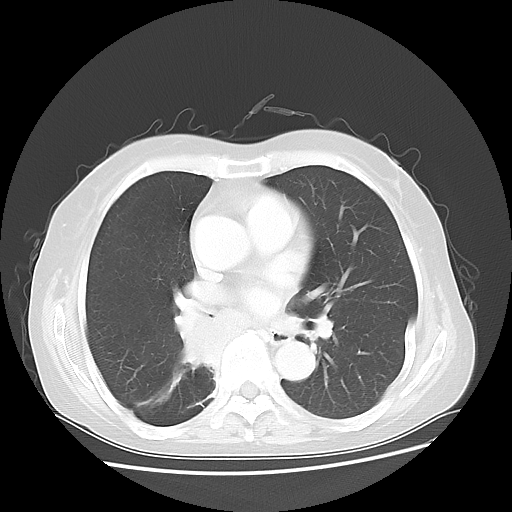
Chest CT, one axial slice; 120 kVp; lung window (W 1500 / L -600 HU); 512 × 512 image matrix, field of view 360 × 360 mm. Female patient, age 63 years. From the clinical record (not read from this slice): clinical TNM (as recorded): T2 N3 M1b.
Structures marked on this image (bounding box drawn by a radiologist):
- lung tumour (recorded histology: small cell carcinoma): bounding box <160,303,233,400> (left, top, right, bottom; pixels)